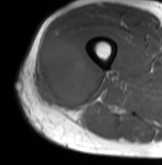
MRI of an extremity soft-tissue mass, one axial slice; slice 34 of 61 in the series (ordered by position); MR volume resampled by the dataset authors to the PET/CT grid (not the native acquisition matrix); 3.27 mm slice thickness; 162 × 165 image matrix, field of view 158 × 161 mm. Male patient. Case-level facts recorded for this patient, not image findings: histological type: poorly differentiated synovial sarcoma; grade: high; site of the primary tumour: right buttock.
Structures marked on this image (expert contour drawn on MRI and transferred to this co-registered scan by the dataset authors):
- gross tumour volume including surrounding oedema: bounding box [x1, y1, x2, y2] px = [34, 36, 97, 105]
- gross tumour volume (mass): [41, 38, 97, 105]